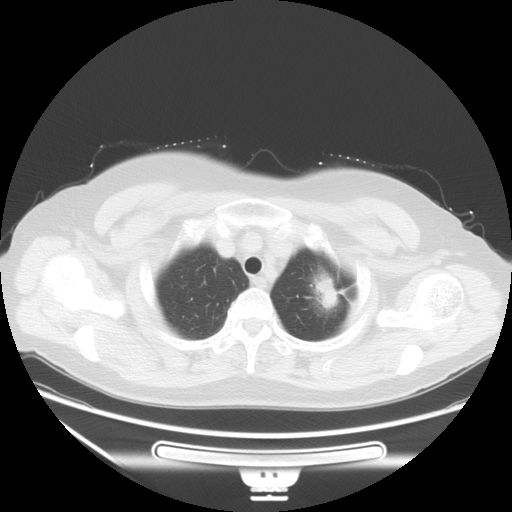
Chest CT, one axial slice. Slice 48 of 53 in the series (ordered by position). Reconstruction kernel STANDARD. 120 kVp. Lung window (W 1500 / L -600 HU). 512 × 512 image matrix, field of view 403 × 403 mm. Patient: female, 66 years. From the clinical record (not read from this slice): clinical TNM (as recorded): T2 N0 M0; histopathological grade: G2.
Annotated regions visible in this slice (bounding box drawn by a radiologist):
- lung tumour (recorded histology: adenocarcinoma): bounding box <301,260,349,324> (left, top, right, bottom; pixels)